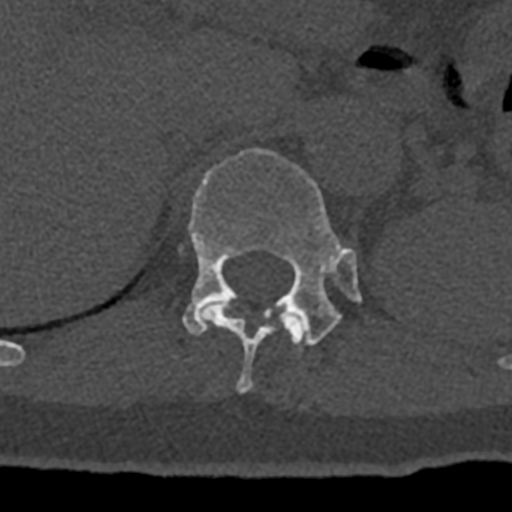
CT including the spine, one axial slice. Position 512 of 797 along the scan axis. Reconstruction kernel Br40s/3. Bone window (W 1800 / L 400 HU). 512 × 512 image matrix, field of view 160 × 160 mm. Patient: male, 74 years. Case-level facts recorded for this patient, not image findings: primary cancer: renal.
Structures marked on this image (semi-automatic segmentation, software-assisted and operator-edited):
- T11 vertebra: bounding box <201,301,304,393> (left, top, right, bottom; pixels)
- T12 vertebra: <182,148,361,346>